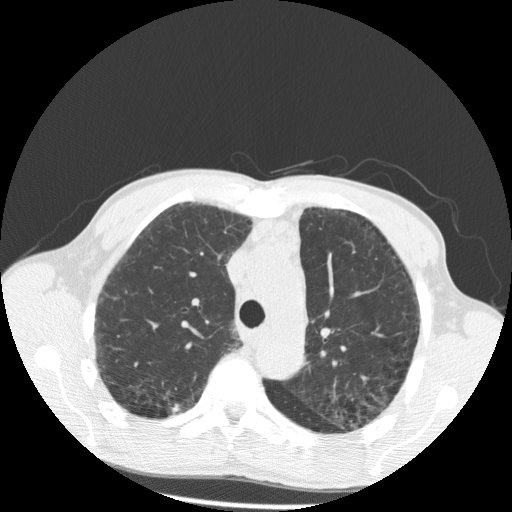
Chest CT (low-dose screening protocol), one axial image. Baseline annual screen. Lung window (W 1500 / L -600 HU). 2.5 mm slice thickness. Slice 133 of 181 in the series. Male participant, aged 60 years at enrolment. Current smoker at enrolment.
Lesion marked by an expert reader, bounding box (x1, y1, x2, y2) in pixels: (162, 397, 188, 421). Screening reader's record for this exam (one nodule recorded; not confirmed to be the boxed lesion): non-calcified nodule or mass ≥4 mm, right lower lobe, 6 × 6 mm, spiculated (stellate) margins, soft tissue attenuation. Official screen result: positive, change unspecified: nodule(s) >= 4 mm or enlarging nodule(s), mass(es), or other non-specific abnormalities suspicious for lung cancer. Participant outcome: lung cancer diagnosed 688 days after this screen (after the second annual screen) — squamous cell carcinoma, NOS, right upper lobe, well differentiated (G1), stage IA (AJCC 6th edition), 15 mm at pathology.